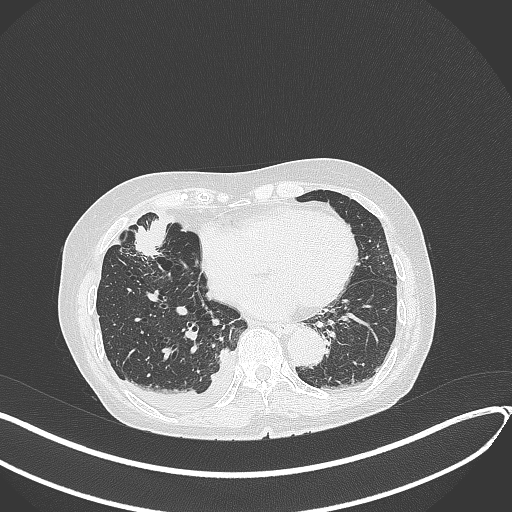
Chest CT, one axial slice. Reconstruction kernel B70f. 120 kVp. Lung window (W 1500 / L -600 HU). 1 mm slice thickness. 512 × 512 image matrix, field of view 400 × 400 mm. Female patient, age 75 years. Case-level facts recorded for this patient, not image findings: clinical TNM (as recorded): T2a N3 M0.
Outlined on this slice (bounding box drawn by a radiologist):
- lung tumour (recorded histology: adenocarcinoma): bounding box [x1, y1, x2, y2] px = [127, 225, 162, 259]